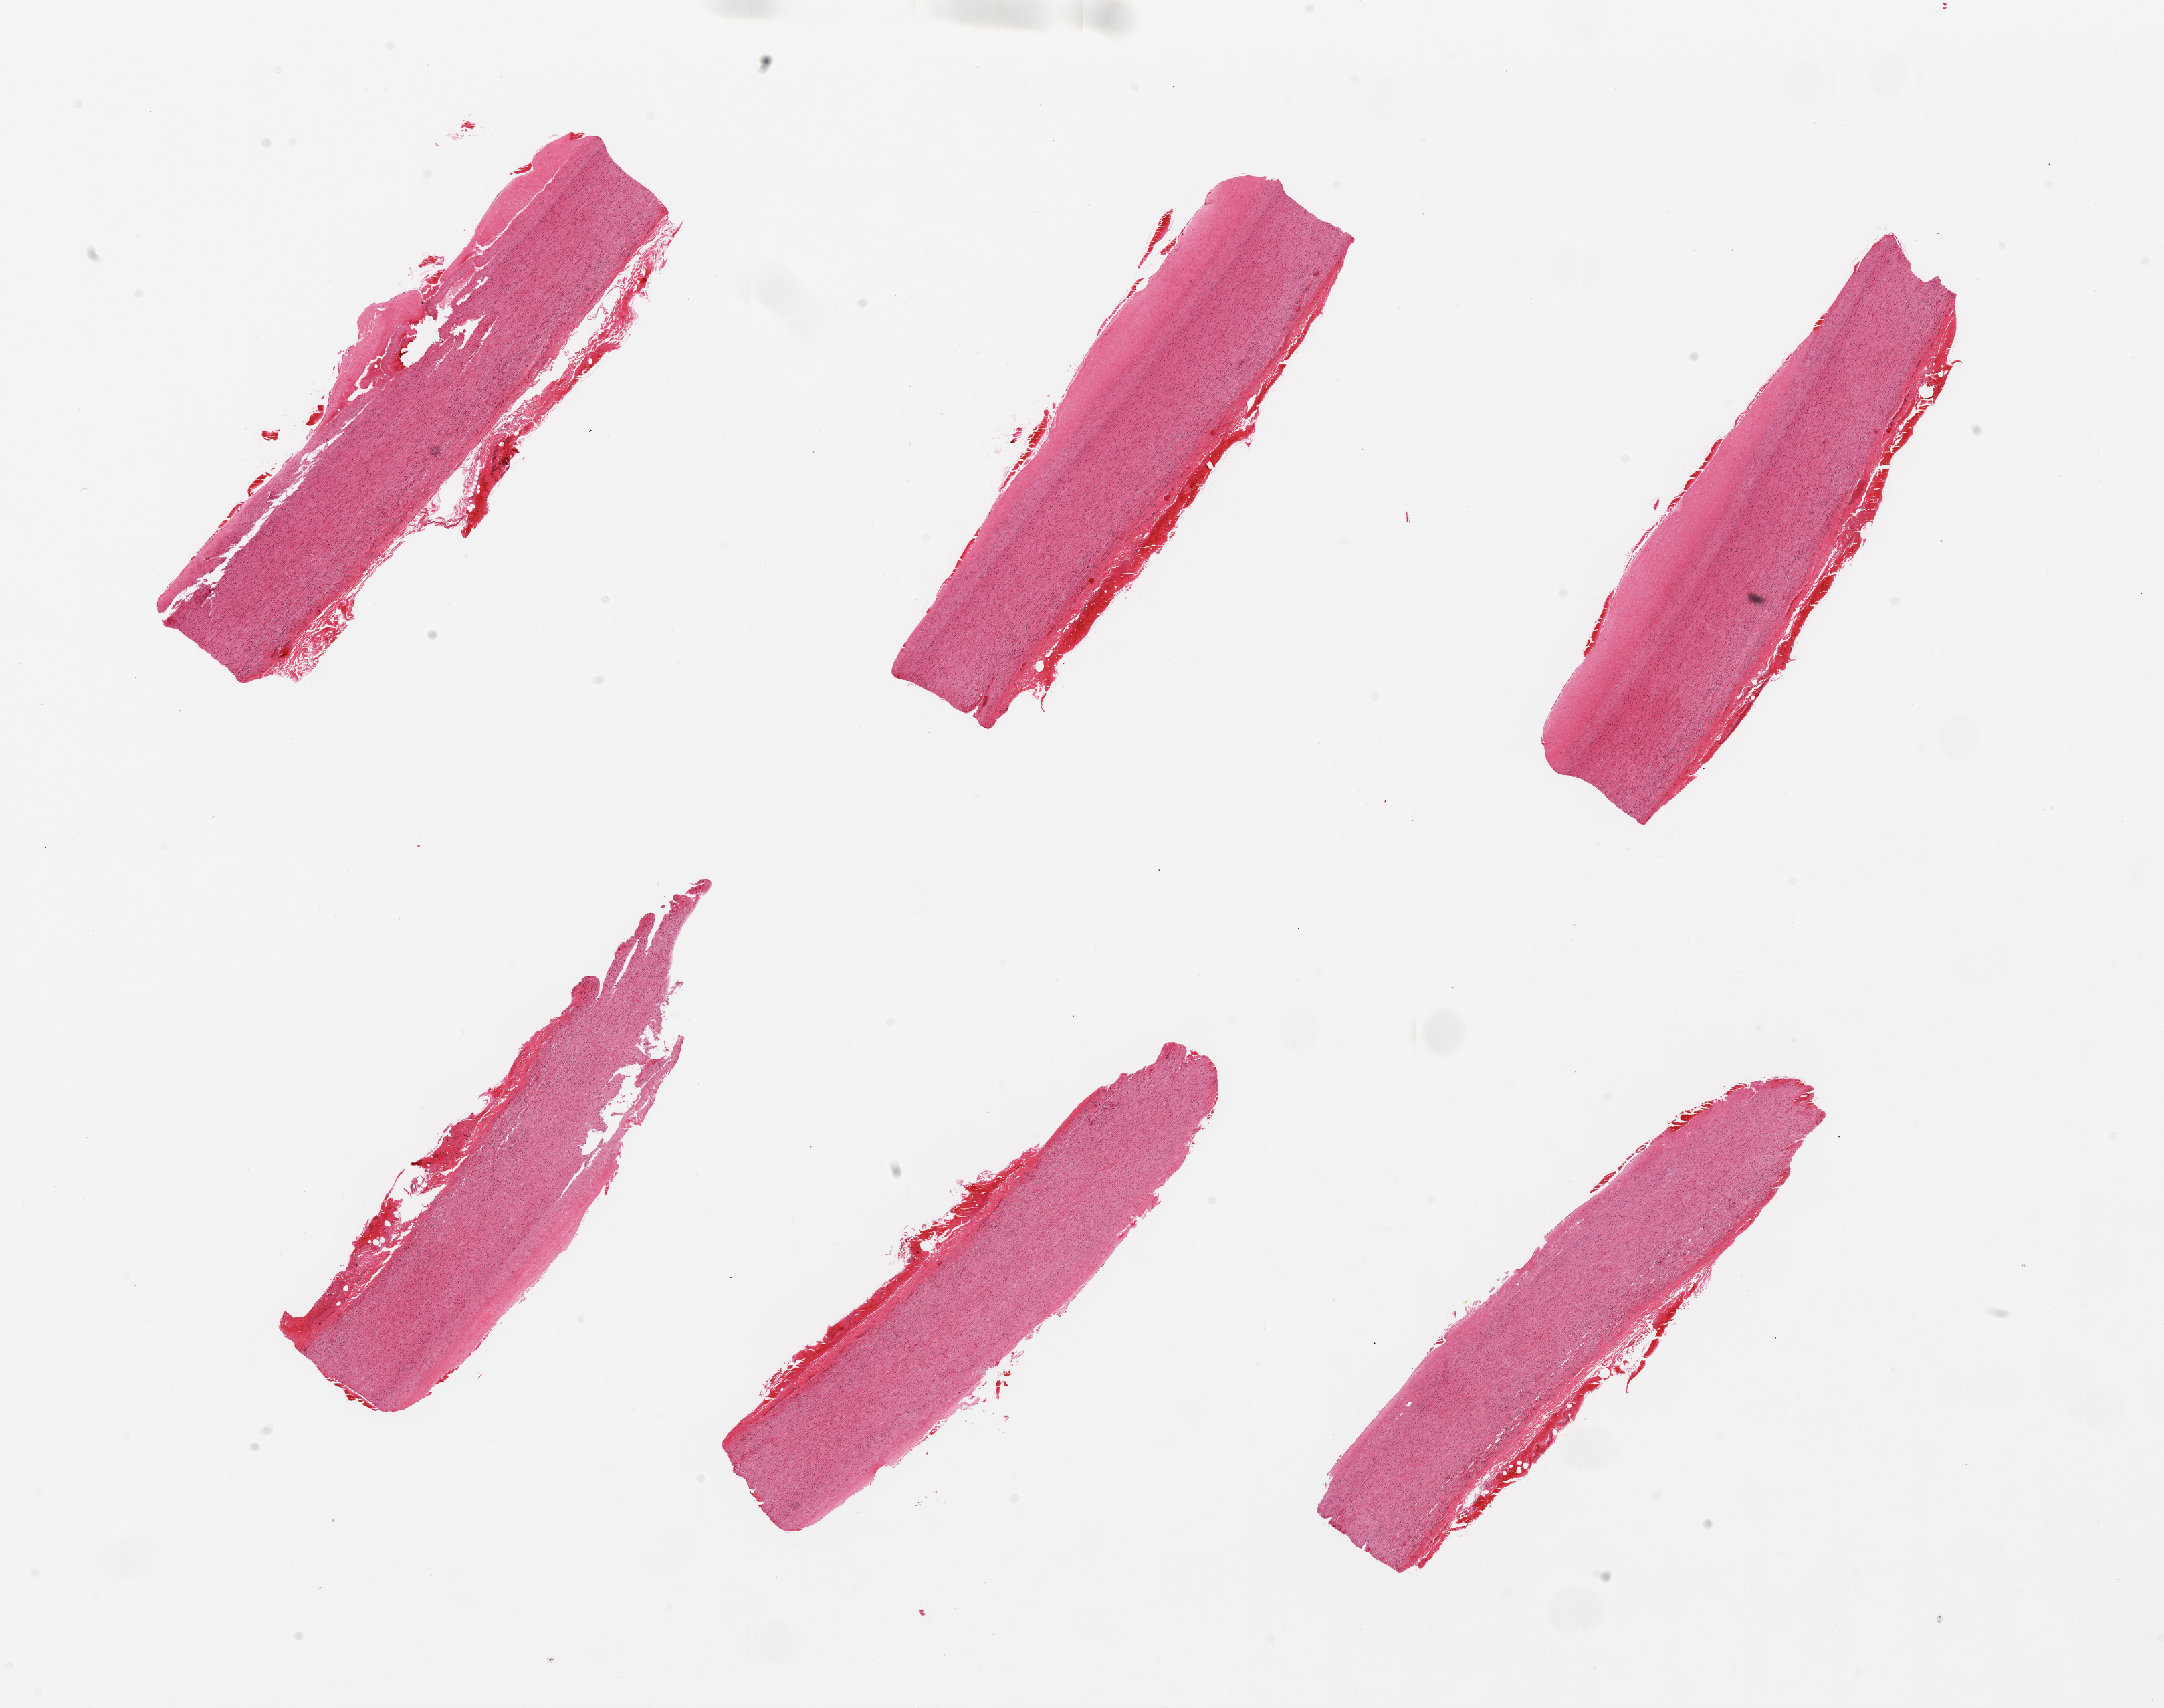
Digitized haematoxylin and eosin-stained section, brightfield, low-resolution overview of the scanned area, about 25.6 x 20.2 mm (slide scanned at 20x), PAXgene-fixed paraffin-embedded (PFPE) section, sampled site (target tissue): aorta, donor tissue sample. Donor: male.
• reviewer comment on this tissue sample: 6 pieces, atherosclerosis with fibrin/mural thrombus